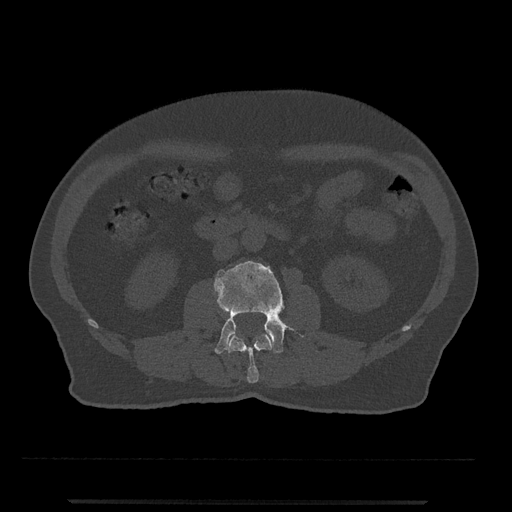
CT including the spine, one axial slice; slice 227 of 797 in the series (ordered by position); reconstruction kernel Br40s/3; bone window (W 1800 / L 400 HU); 512 × 512 image matrix, field of view 419 × 419 mm. Male patient, age 63 years. From the clinical record (not read from this slice): primary cancer: prostate.
Structures marked on this image (semi-automatic segmentation, software-assisted and operator-edited):
- L2 vertebra: bounding box (x1, y1, x2, y2) in pixels: (227, 333, 273, 383)
- L3 vertebra: (214, 261, 303, 354)